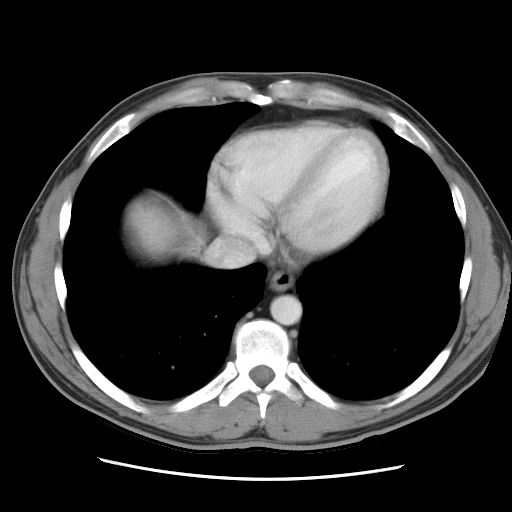
Contrast-enhanced abdominal CT, one axial slice; position 28 of 34 along the scan axis; intravenous contrast given; soft-tissue window (W 400 / L 40 HU); 512 × 512 image matrix. Male patient, age 40 years. Case-level facts recorded for this patient, not image findings: diagnosis: colorectal cancer liver metastases, imaged before liver resection; multiple liver metastases: yes; largest metastasis: 1.5 cm; chemotherapy before resection: no.
Annotated regions visible in this slice (expert manual segmentation):
- liver: box from (x=123, y=195) to (x=191, y=261) px
- planned liver remnant (the part of the liver to remain after resection): (x=123, y=196)–(x=191, y=263)